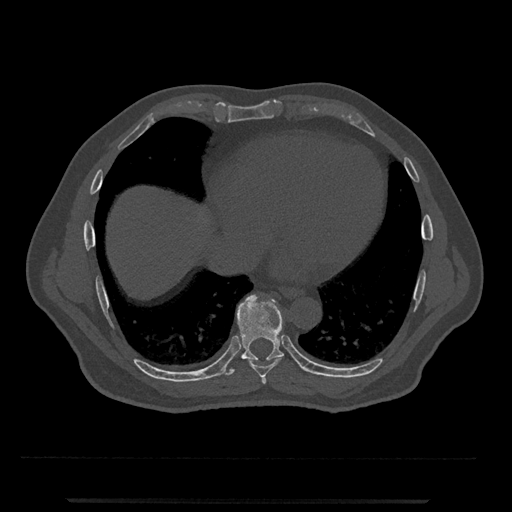
CT including the spine, one axial slice; position 599 of 797 along the scan axis; reconstruction kernel Br40s/3; 120 kVp; bone window (W 1800 / L 400 HU); 512 × 512 image matrix. Male patient, age 63 years. Case-level facts recorded for this patient, not image findings: primary cancer: prostate.
Structures marked on this image (semi-automatically segmented with operator editing):
- T7 vertebra: bounding box <261,375,267,384> (left, top, right, bottom; pixels)
- T8 vertebra: <249,358,281,377>
- T9 vertebra: <221,295,284,376>